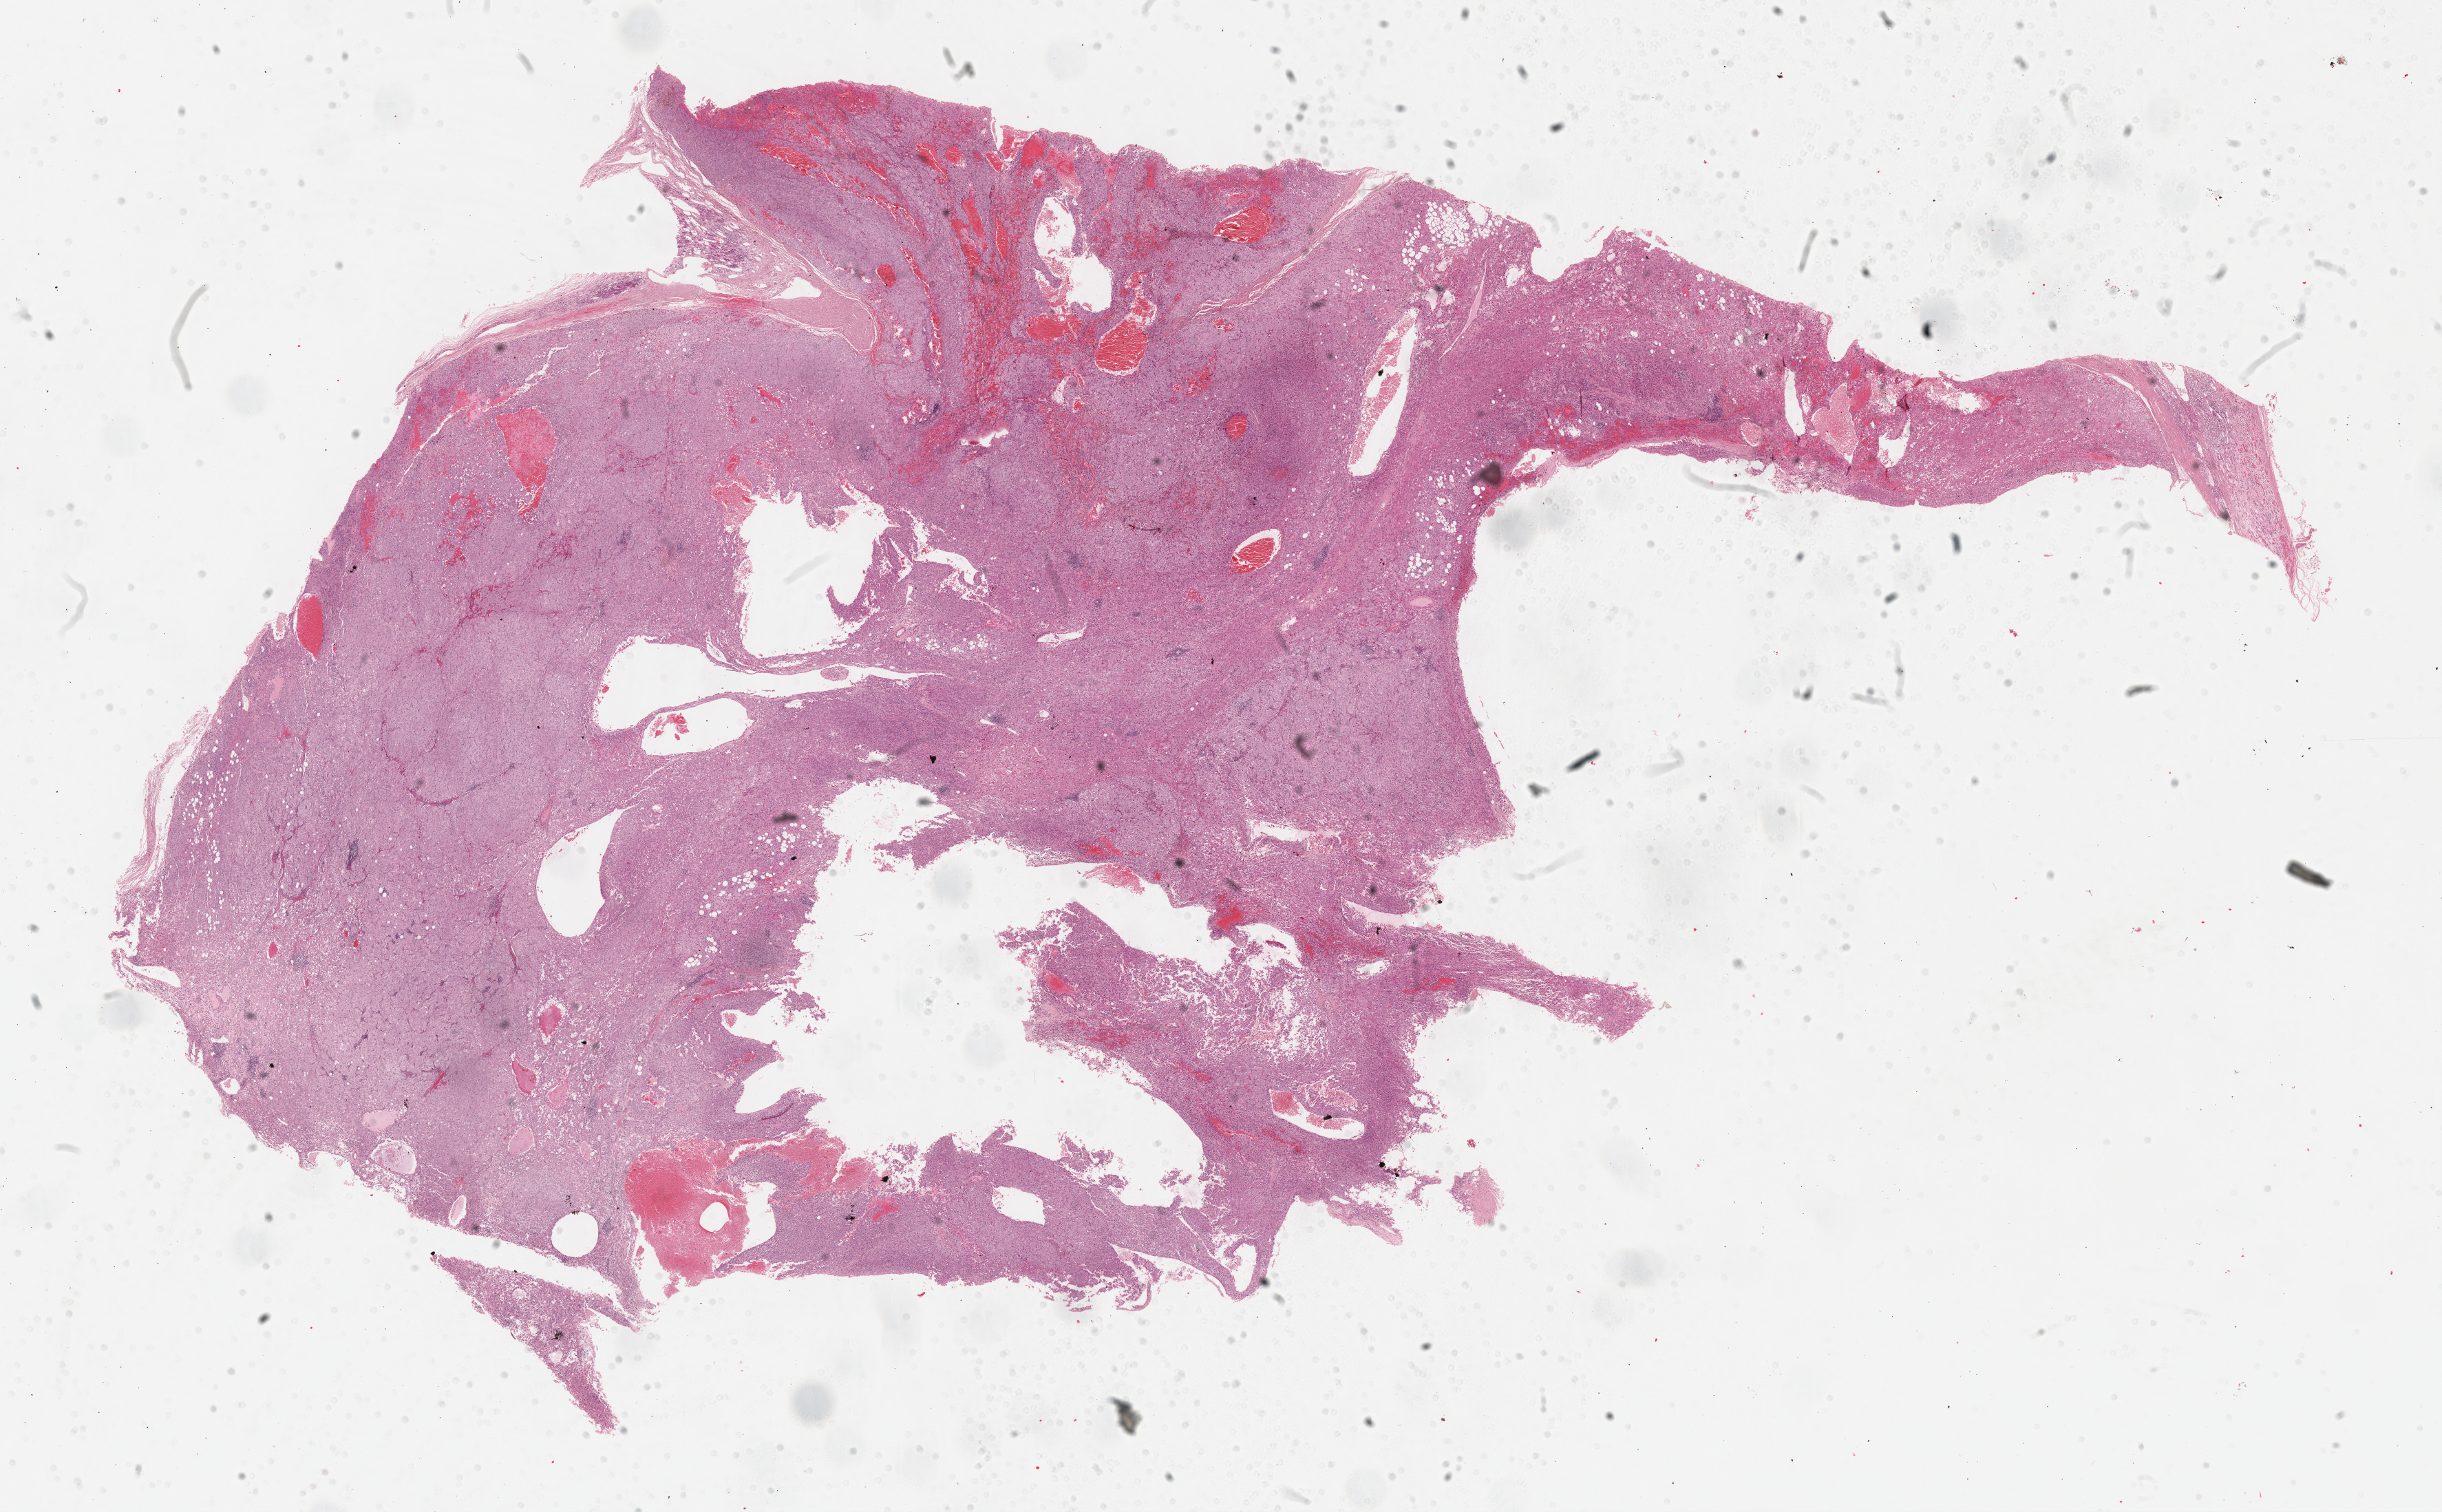
Whole-slide histology image, Hematoxylin and eosin (H&E) stained, a low-resolution overview of the entire scanned area, about 28.7 x 17.8 mm (from a 40x scan); formalin-fixed paraffin-embedded (FFPE) diagnostic section; sample: primary tumour, adrenal cortex. Patient: male, age at initial diagnosis 22 years.
Laterality: right. Histologic diagnosis: Adrenal cortical carcinoma.